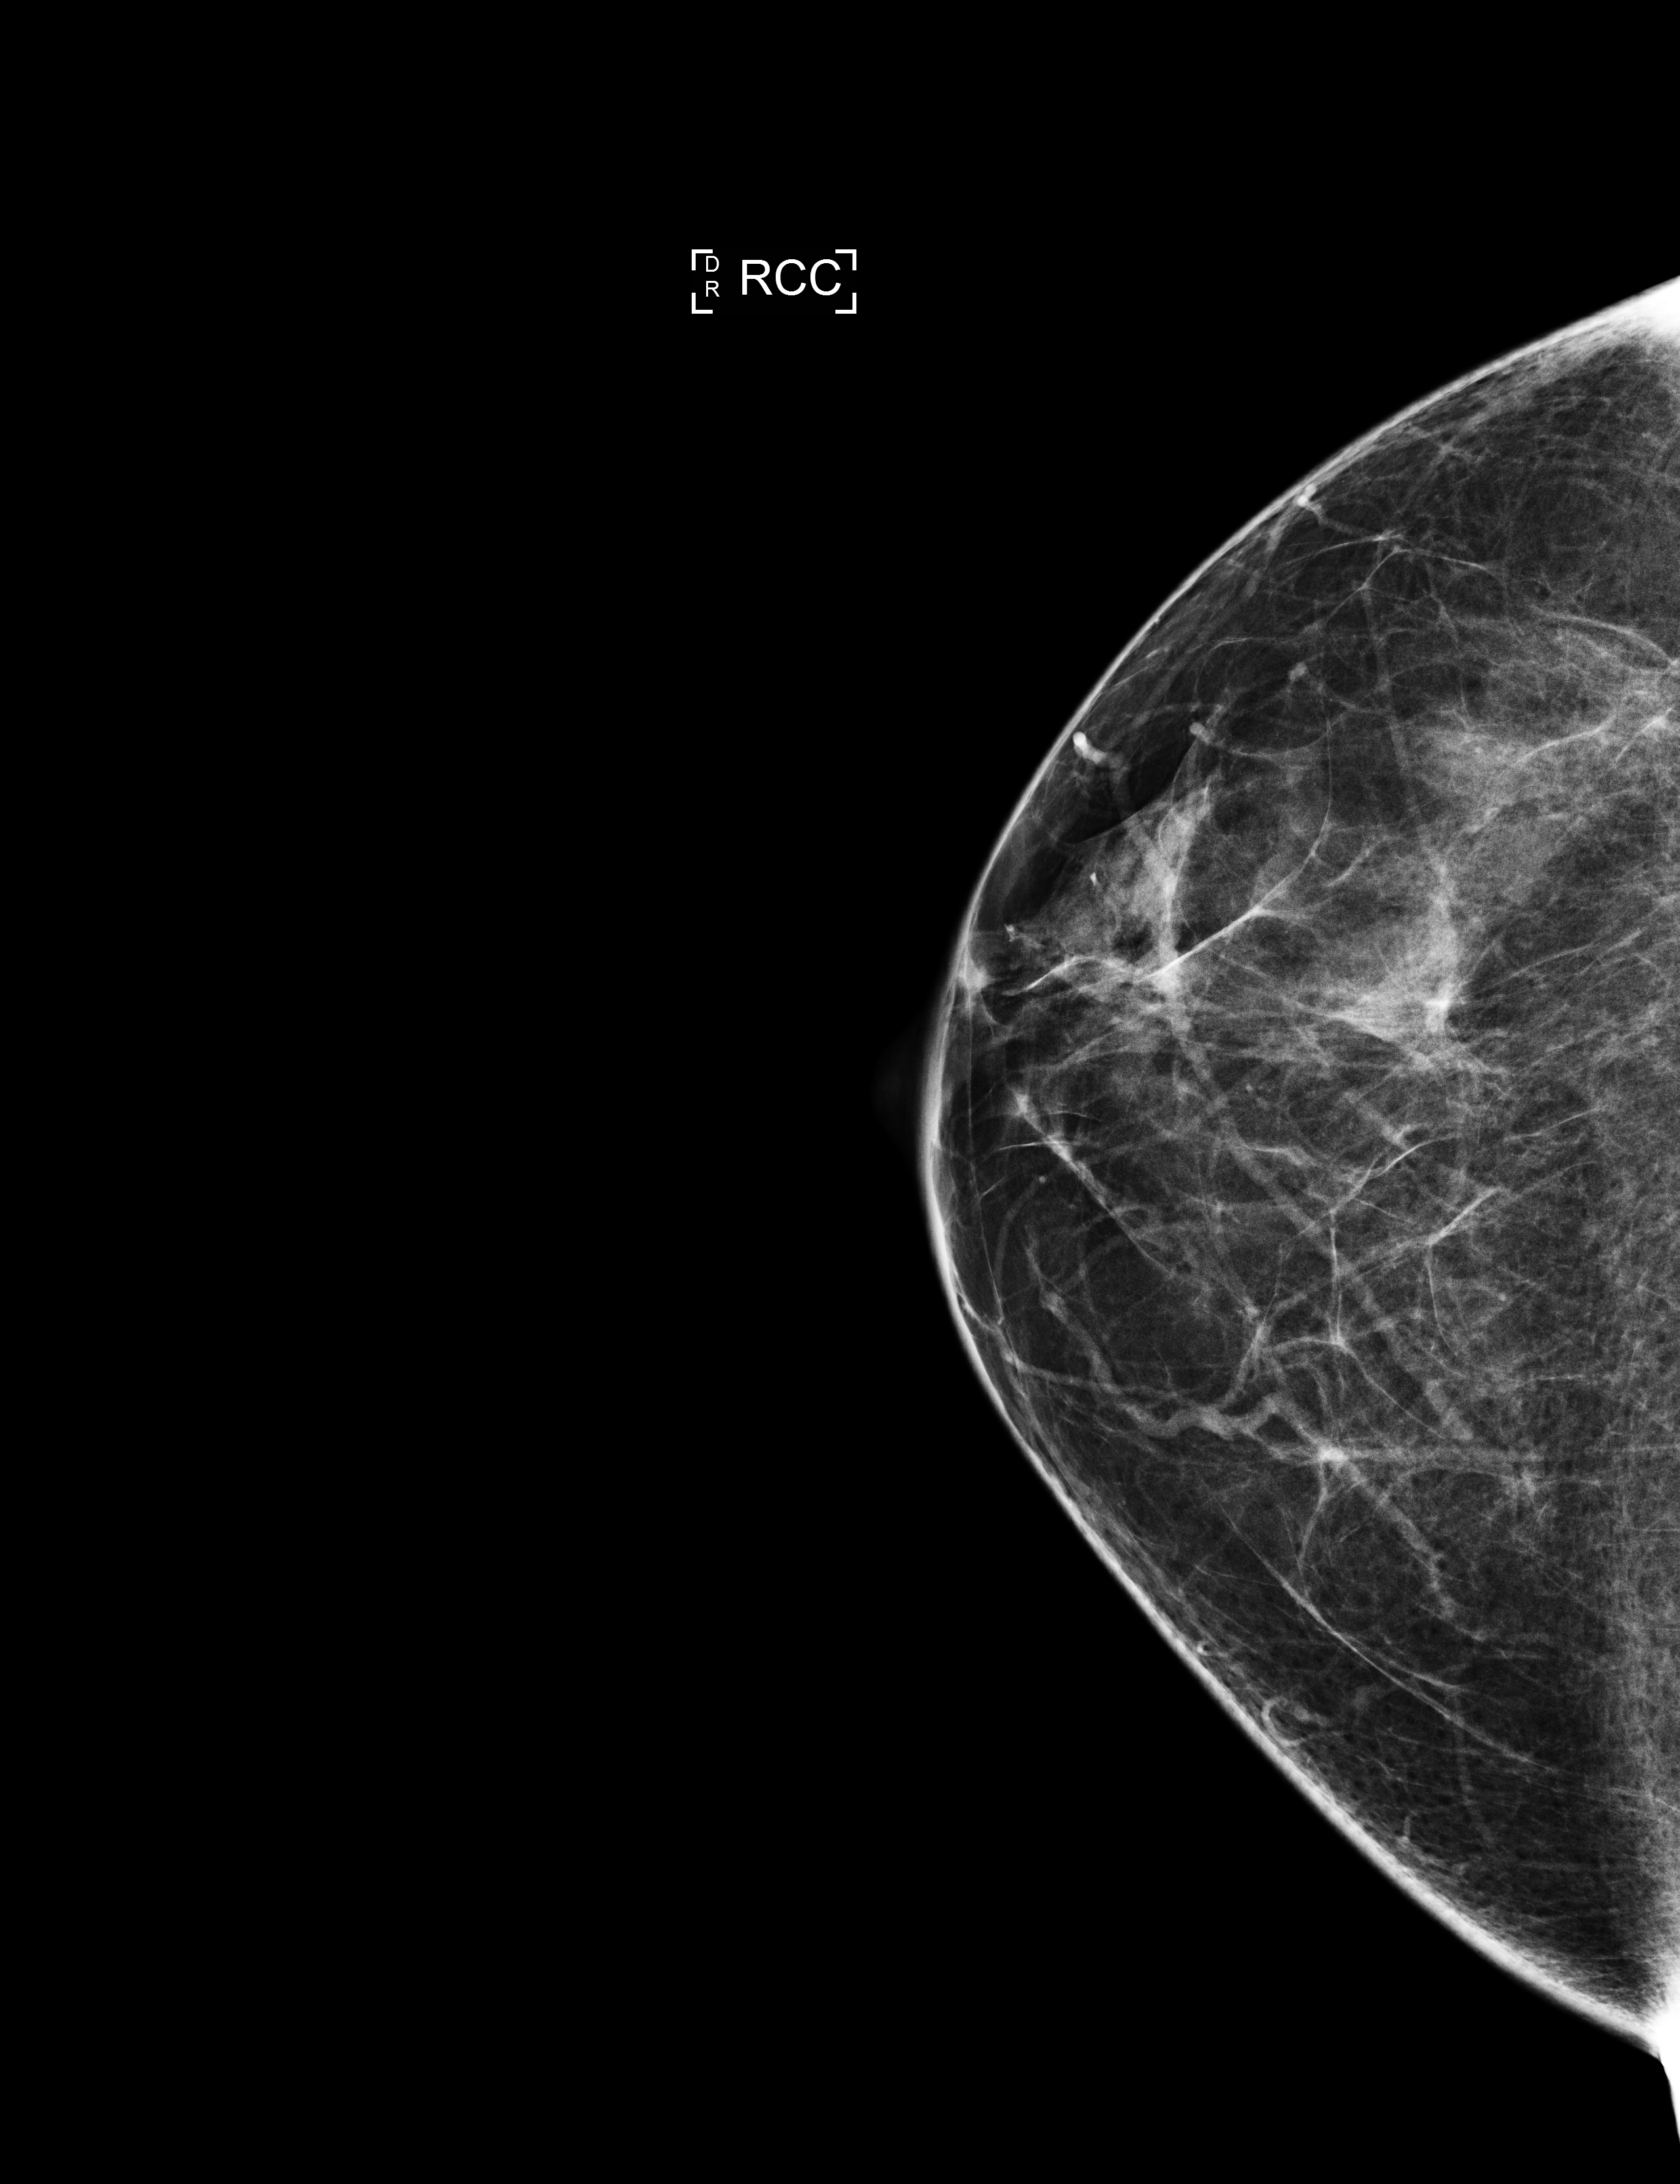
Digital mammogram (FFDM); right breast; CC view; annual screening mammography examination; compressed breast thickness 58 mm; system: Selenia Dimensions. Patient aged 56 years (female).
Final BI-RADS category for the screening round (tomosynthesis exam, both breasts): category 1.